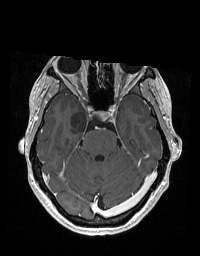
Brain MRI from a brain-tumour surgery series, one axial slice; position 125 of 192 along the scan axis; T1-weighted post-contrast; 1 mm slice thickness; 200 × 256 image matrix, field of view 195 × 250 mm. From the clinical record (not read from this slice): histopathology: Glioblastoma; WHO grade: 2; IDH mutation: no; tumour location: Right Skull Base Temporal.
Structures marked on this image (outlined manually by an expert reader):
- tumour: box from (x=71, y=111) to (x=101, y=133) px